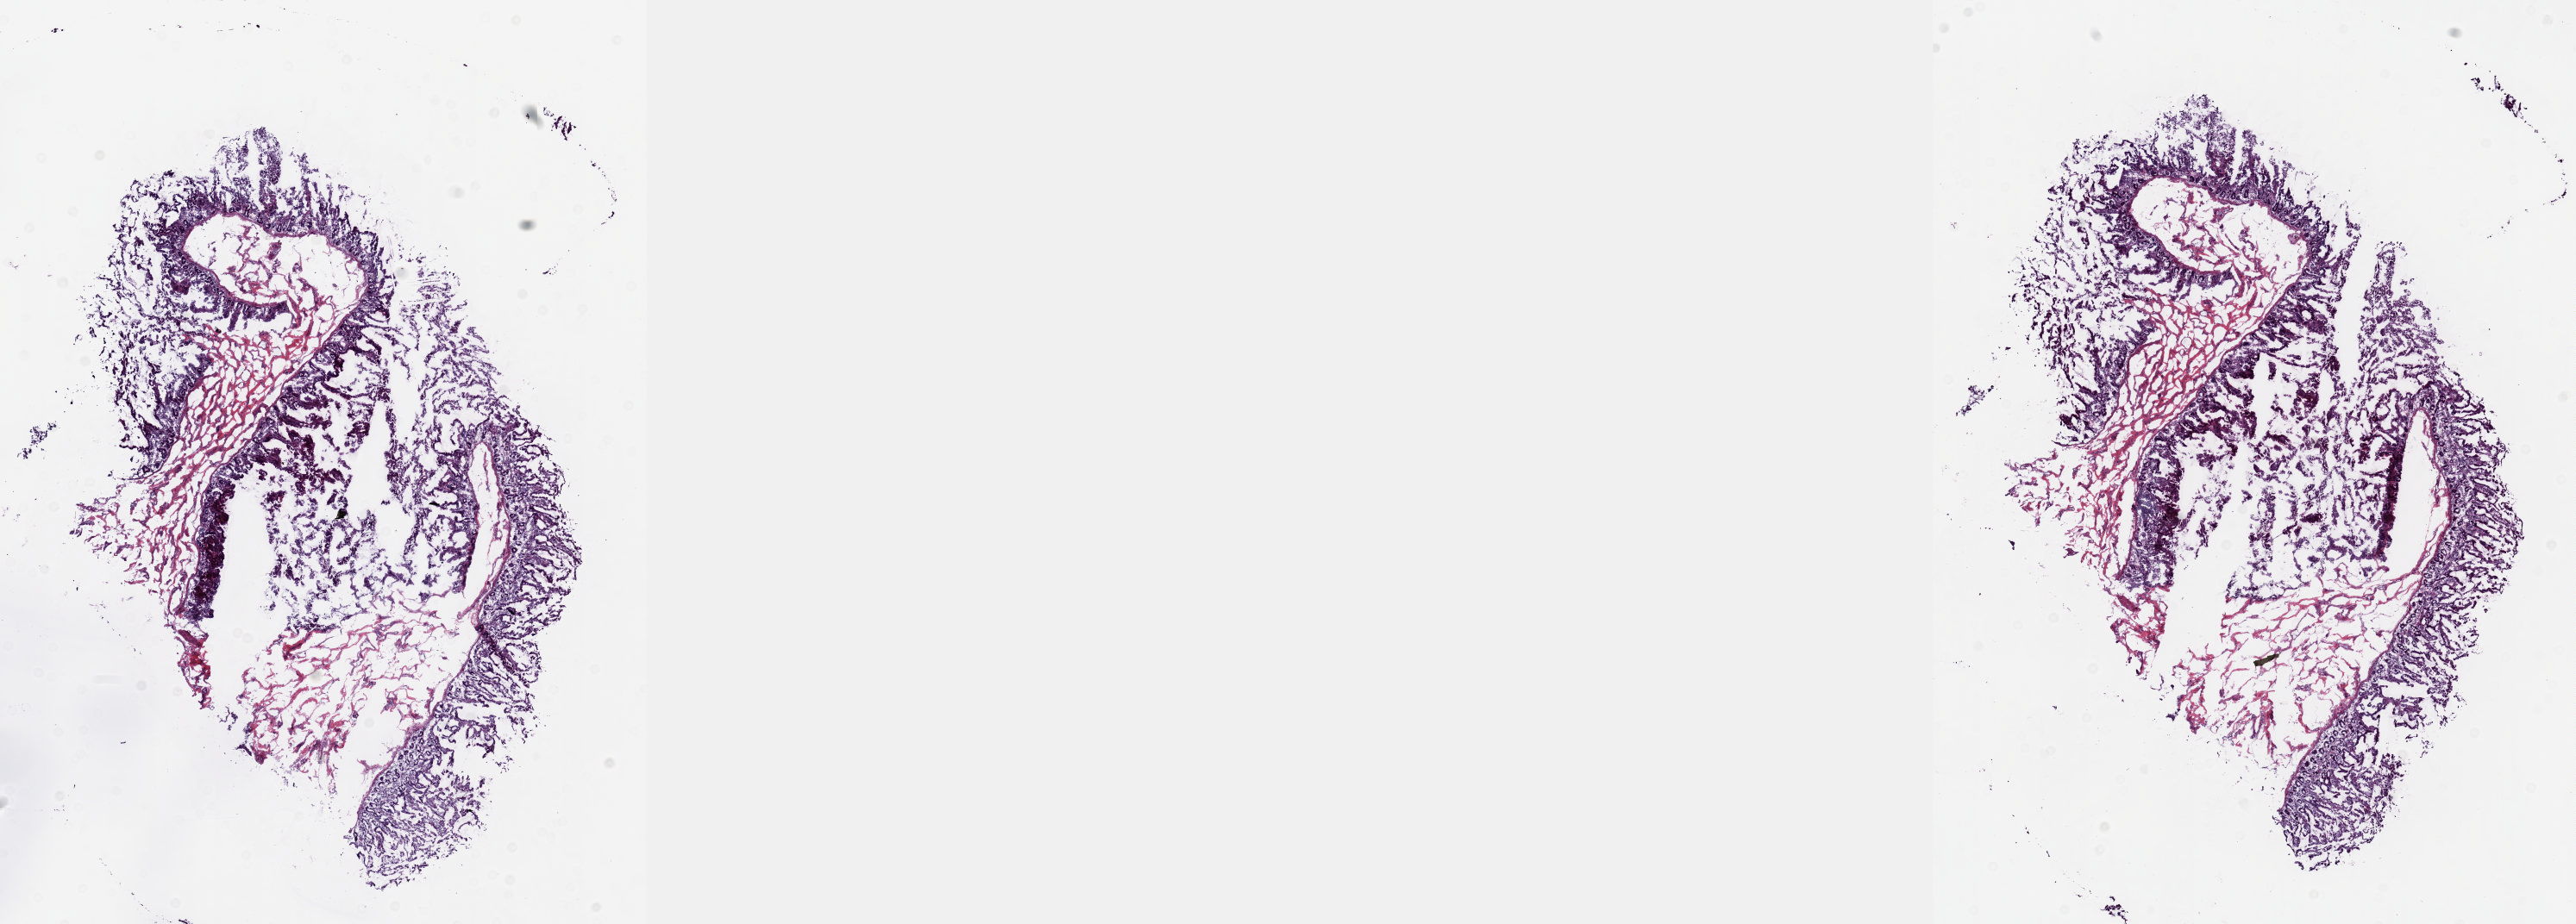
H&E-stained whole-slide image, shown as a low-resolution overview of the whole scanned area (about 24.1 x 8.6 mm). Frozen section. Pancreas, solid tissue normal (non-tumour tissue) sample. Patient: female, age at initial diagnosis 62 years. Slide review estimates, as recorded: tumour cells 0%, tumour nuclei 0%, normal cells 70%, stromal cells 30%, necrosis 0%. Inflammatory infiltration, as recorded: lymphocyte infiltration 70%, monocyte infiltration 10%, neutrophil infiltration 10%.
* this section: solid tissue normal (non-tumour) sample from the same patient
* patient diagnosis: Infiltrating duct carcinoma, NOS (head of pancreas)